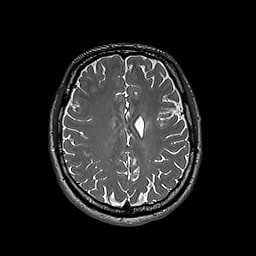
Brain MRI from a brain-tumour surgery series, one axial slice; 1 mm slice thickness; 256 × 256 image matrix. From the clinical record (not read from this slice): histopathology: Oligodendroglioma; WHO grade: 3; IDH mutation: yes; tumour location: Left Frontal.
Outlined on this slice (expert manual segmentation):
- tumour: bounding box <145,119,153,128> (left, top, right, bottom; pixels)